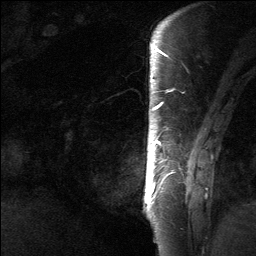
Breast MRI (dynamic contrast-enhanced), one sagittal slice; position 13 of 64 along the scan axis; dynamic contrast-enhanced study with each time point stored as its own series, time point 2 of 3 at this slice position (early post-contrast, ordered by acquisition time); 1.5 T; TE 4.8 ms, TR 27 ms; 2 mm slice thickness; 256 × 256 image matrix, field of view 180 × 180 mm. Patient: female, 39 years. From the clinical record (not read from this slice): setting: breast cancer imaged before/during neoadjuvant chemotherapy; receptor status: HER2-positive.
Outlined on this slice (semi-automatic segmentation, software-assisted and operator-edited):
- analysis volume of interest (the breast-tissue region the enhancement analysis was run in; not a lesion): bounding box <143,40,201,217> (left, top, right, bottom; pixels)
- tumour enhancement mask (voxels above the 90 % enhancement threshold inside the analysis volume of interest): <144,49,165,200>